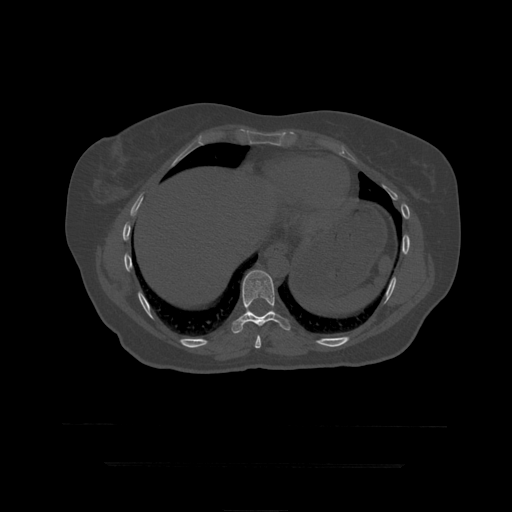
CT including the spine, one axial slice; slice 243 of 399 in the series (ordered by position); bone window (W 1800 / L 400 HU); 1.25 mm slice thickness; 512 × 512 image matrix, field of view 450 × 450 mm. Patient age 41 years. Case-level facts recorded for this patient, not image findings: primary cancer: breast.
Structures marked on this image (semi-automatic segmentation, software-assisted and operator-edited):
- T10 vertebra: box from (x=232, y=270) to (x=291, y=334) px
- T9 vertebra: (x=255, y=335)–(x=262, y=350)